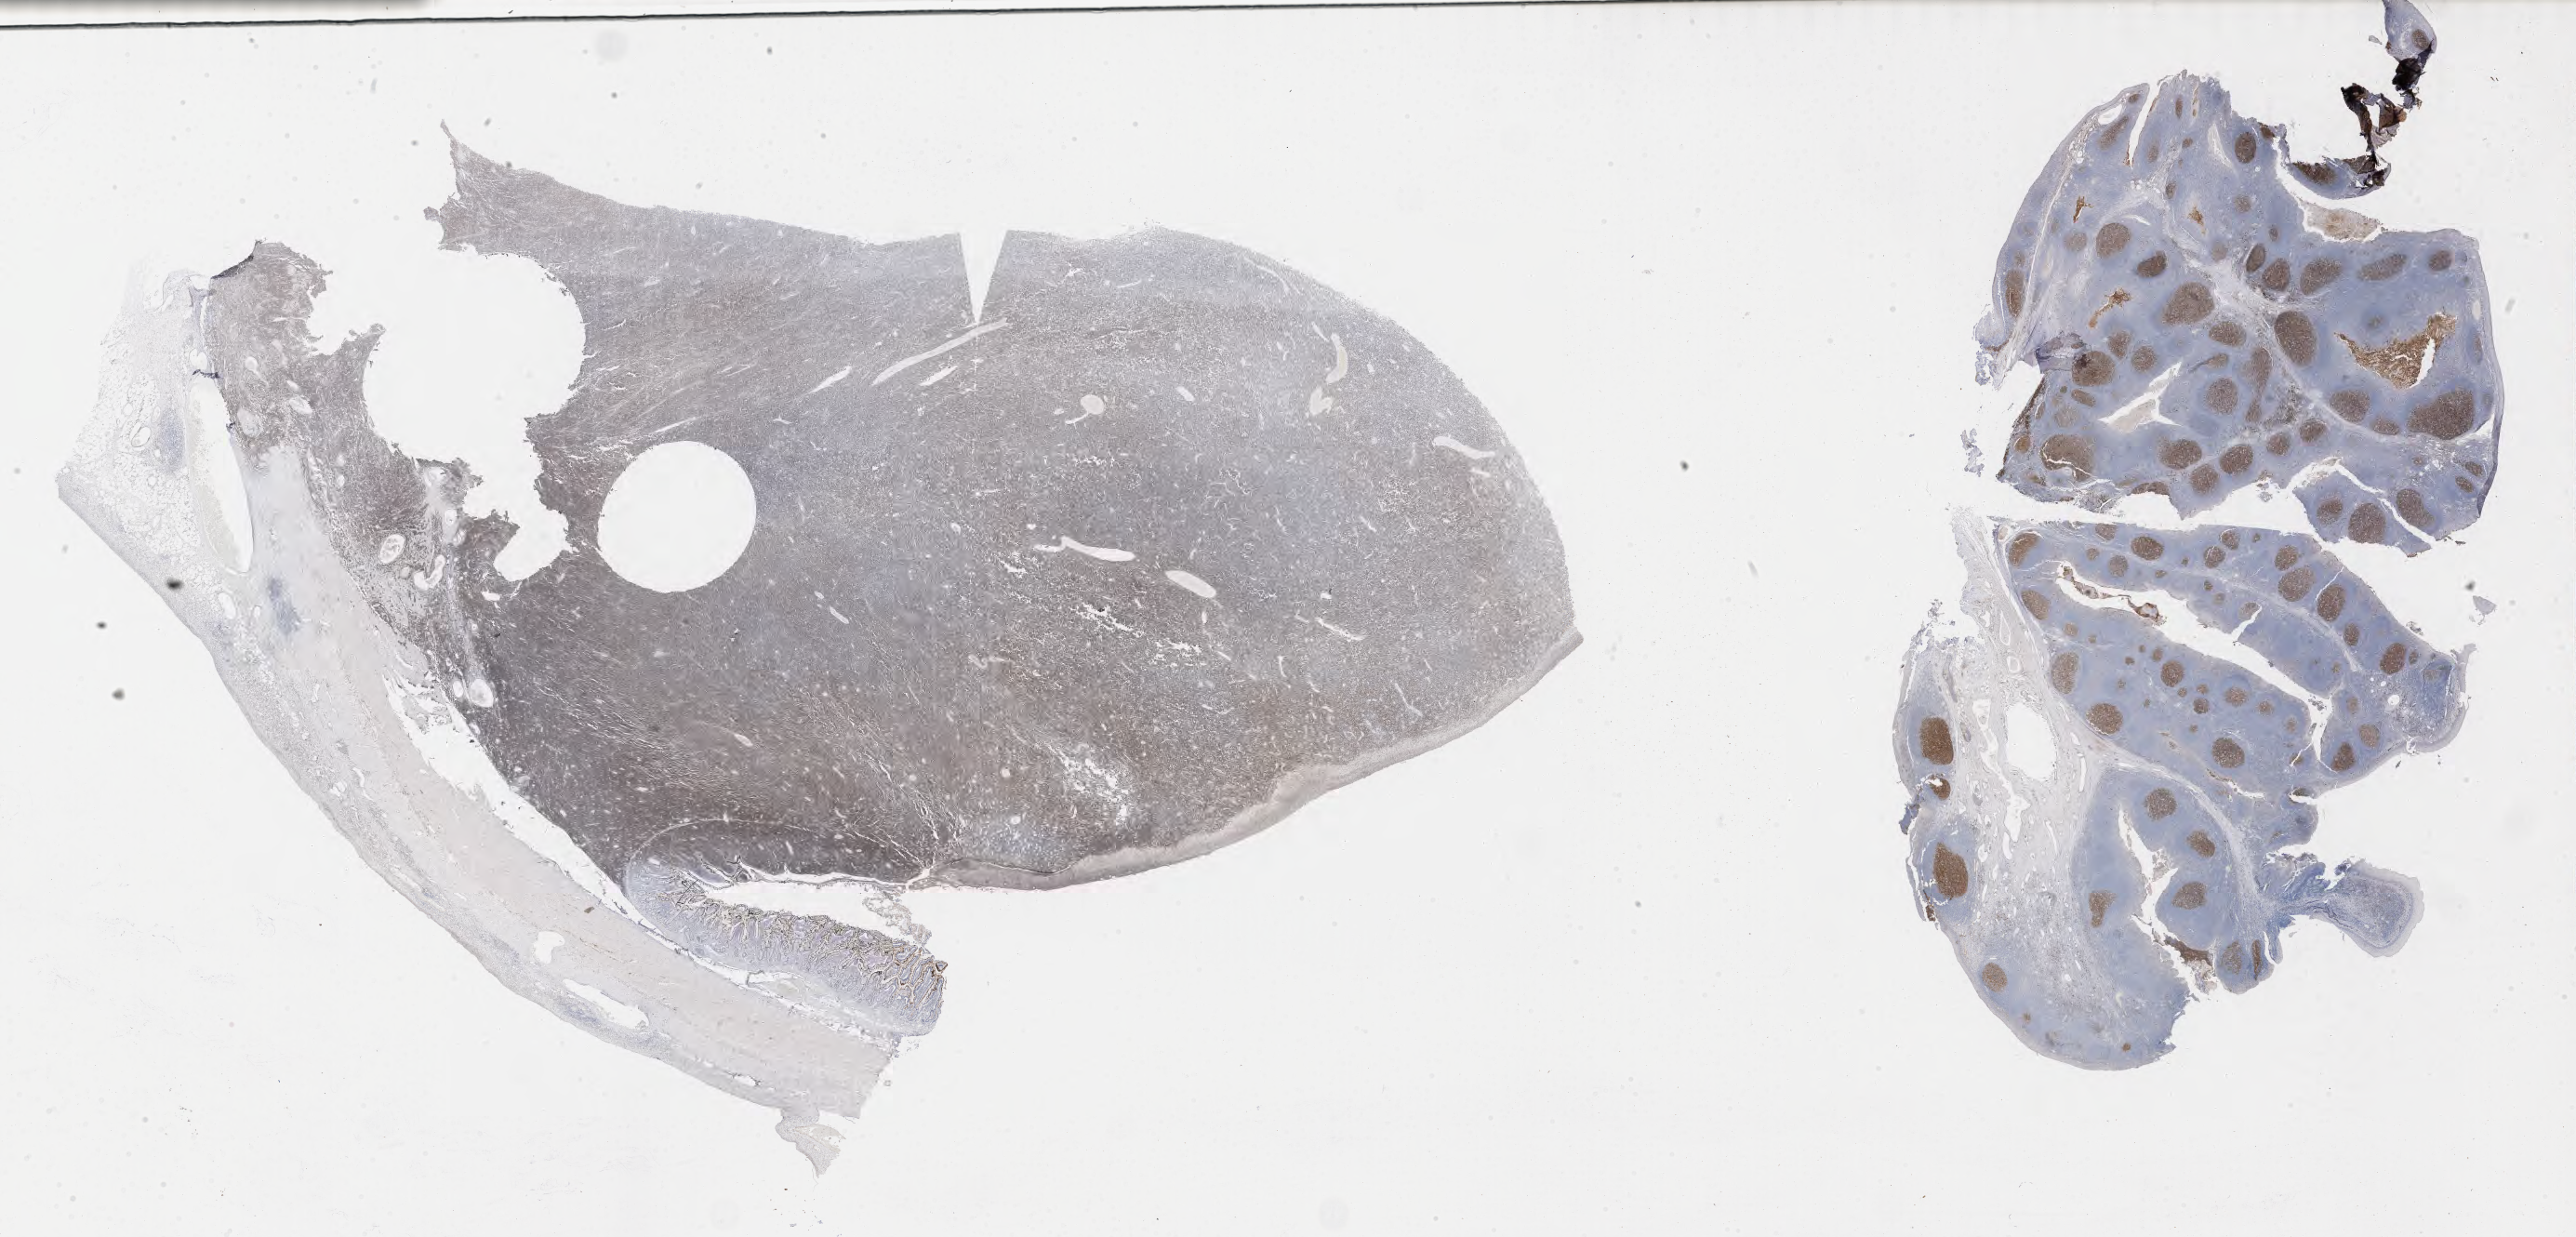
Immunohistochemistry (IHC) whole-slide image stained for CD10 — low-resolution overview of the scanned area, about 44.8 x 21.5 mm, tumor tissue. Female patient, 15 years old.
Histologic diagnosis: Burkitt lymphoma, NOS.